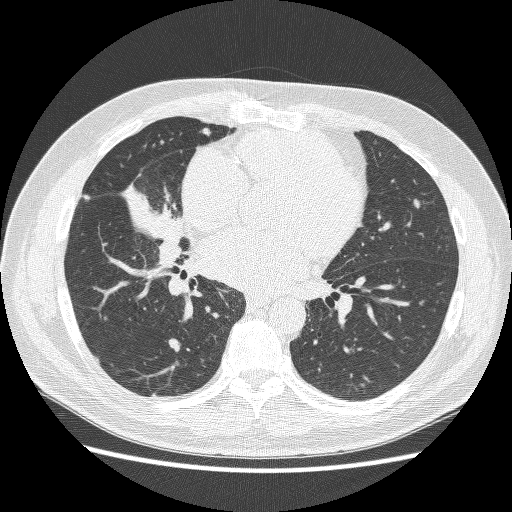
Axial slice from a low-dose chest CT screening exam, baseline screening round, lung window (W 1500 / L -600 HU), 1.25 mm slice thickness, lung (sharp) reconstruction kernel (BONE), 120 kVp. Male, age 59 years at enrolment.
• Expert reader's lesion annotation, bounding box <114,168,196,251> (left, top, right, bottom; pixels).
• No non-calcified nodule or mass ≥4 mm was recorded by the screening reader at this exam.
• Participant outcome: lung cancer diagnosed 24 days after this screen — adenocarcinoma, NOS, right middle lobe, poorly differentiated (G3), stage IV (AJCC 6th edition), 54 mm at pathology.